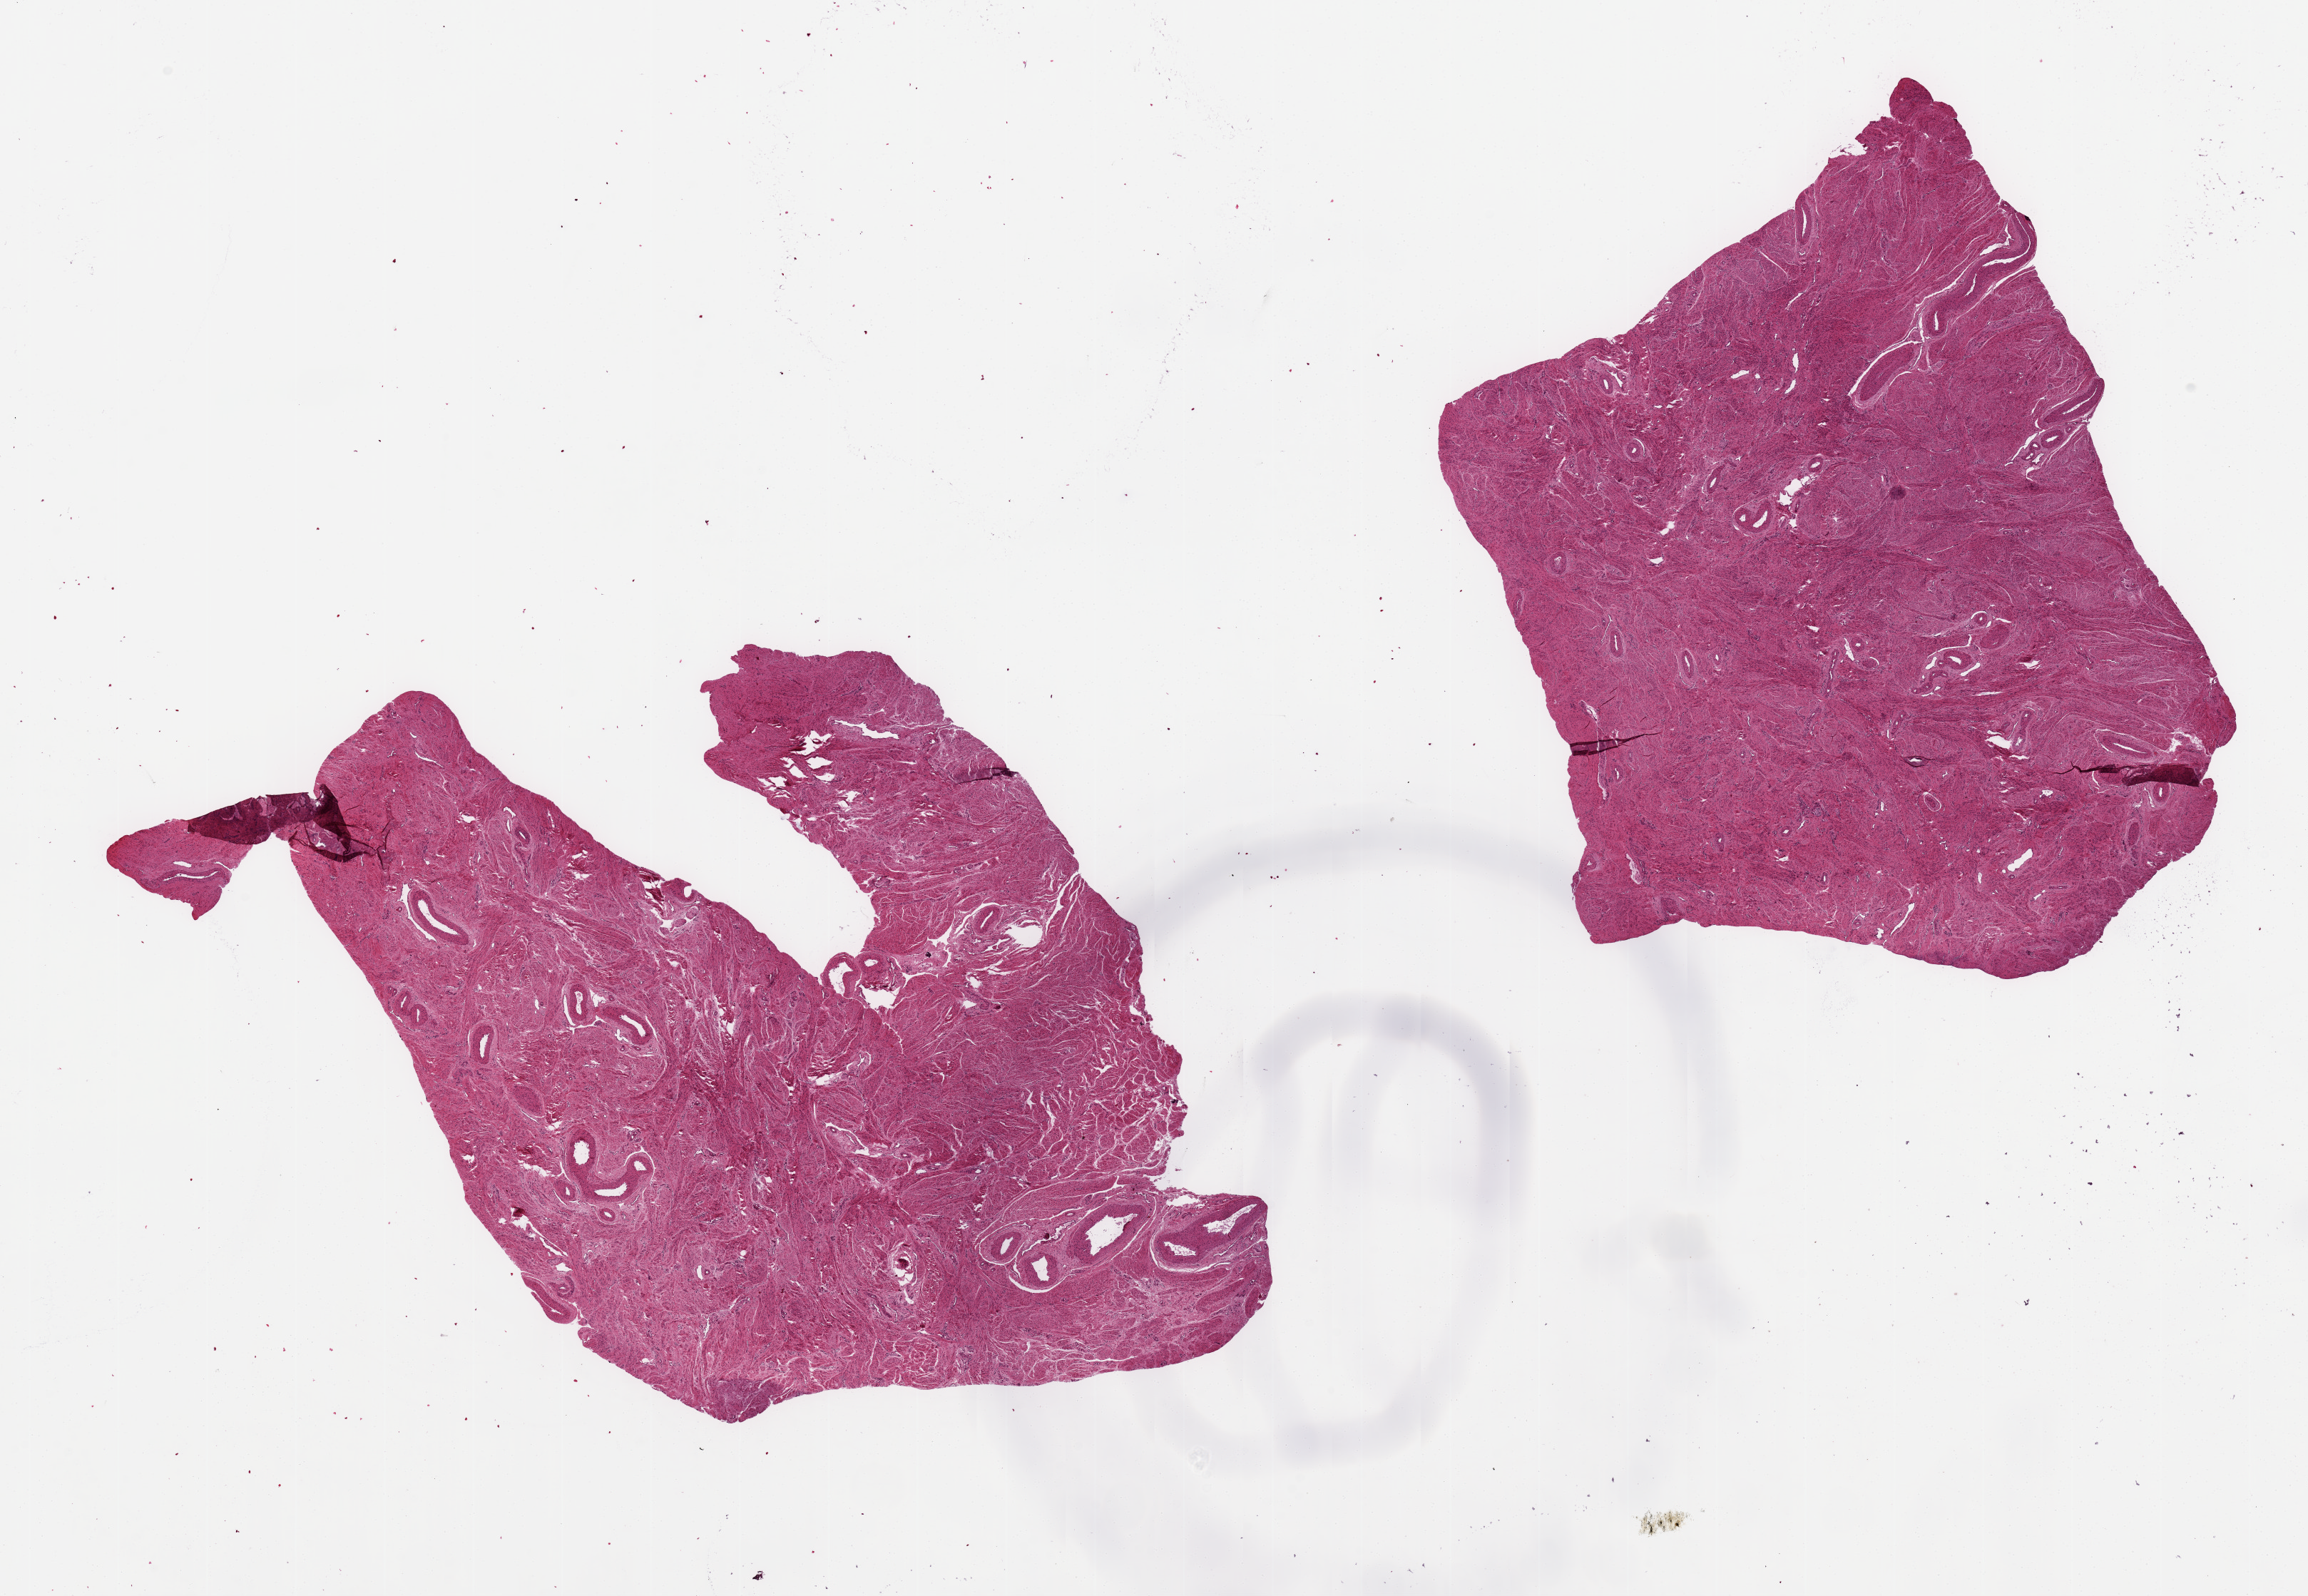
Hematoxylin and eosin (H&E) whole-slide image — a low-resolution overview of the entire scanned area, about 25.6 x 17.7 mm; PAXgene-fixed, paraffin-embedded tissue; sampled site (target tissue): uterus; donor tissue sample. Female donor.
Pathologist's review note for this sample: 2 pieces ~8 x 7mm; No endometrium , only myometium.